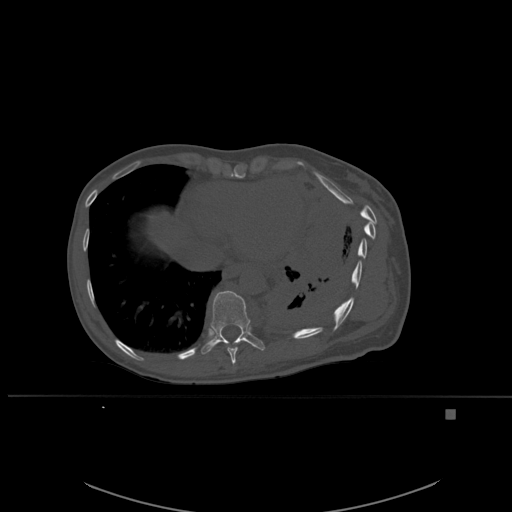
CT including the spine, one axial slice; slice 323 of 537 in the series (ordered by position); bone window (W 1800 / L 400 HU); 1.5 mm slice thickness; 512 × 512 image matrix, field of view 440 × 440 mm. Patient: female, 45 years. Case-level facts recorded for this patient, not image findings: primary cancer: lung.
Annotated regions visible in this slice (semi-automatic segmentation, software-assisted and operator-edited):
- T10 vertebra: bounding box [x1, y1, x2, y2] px = [201, 290, 265, 355]
- T9 vertebra: [224, 341, 238, 365]